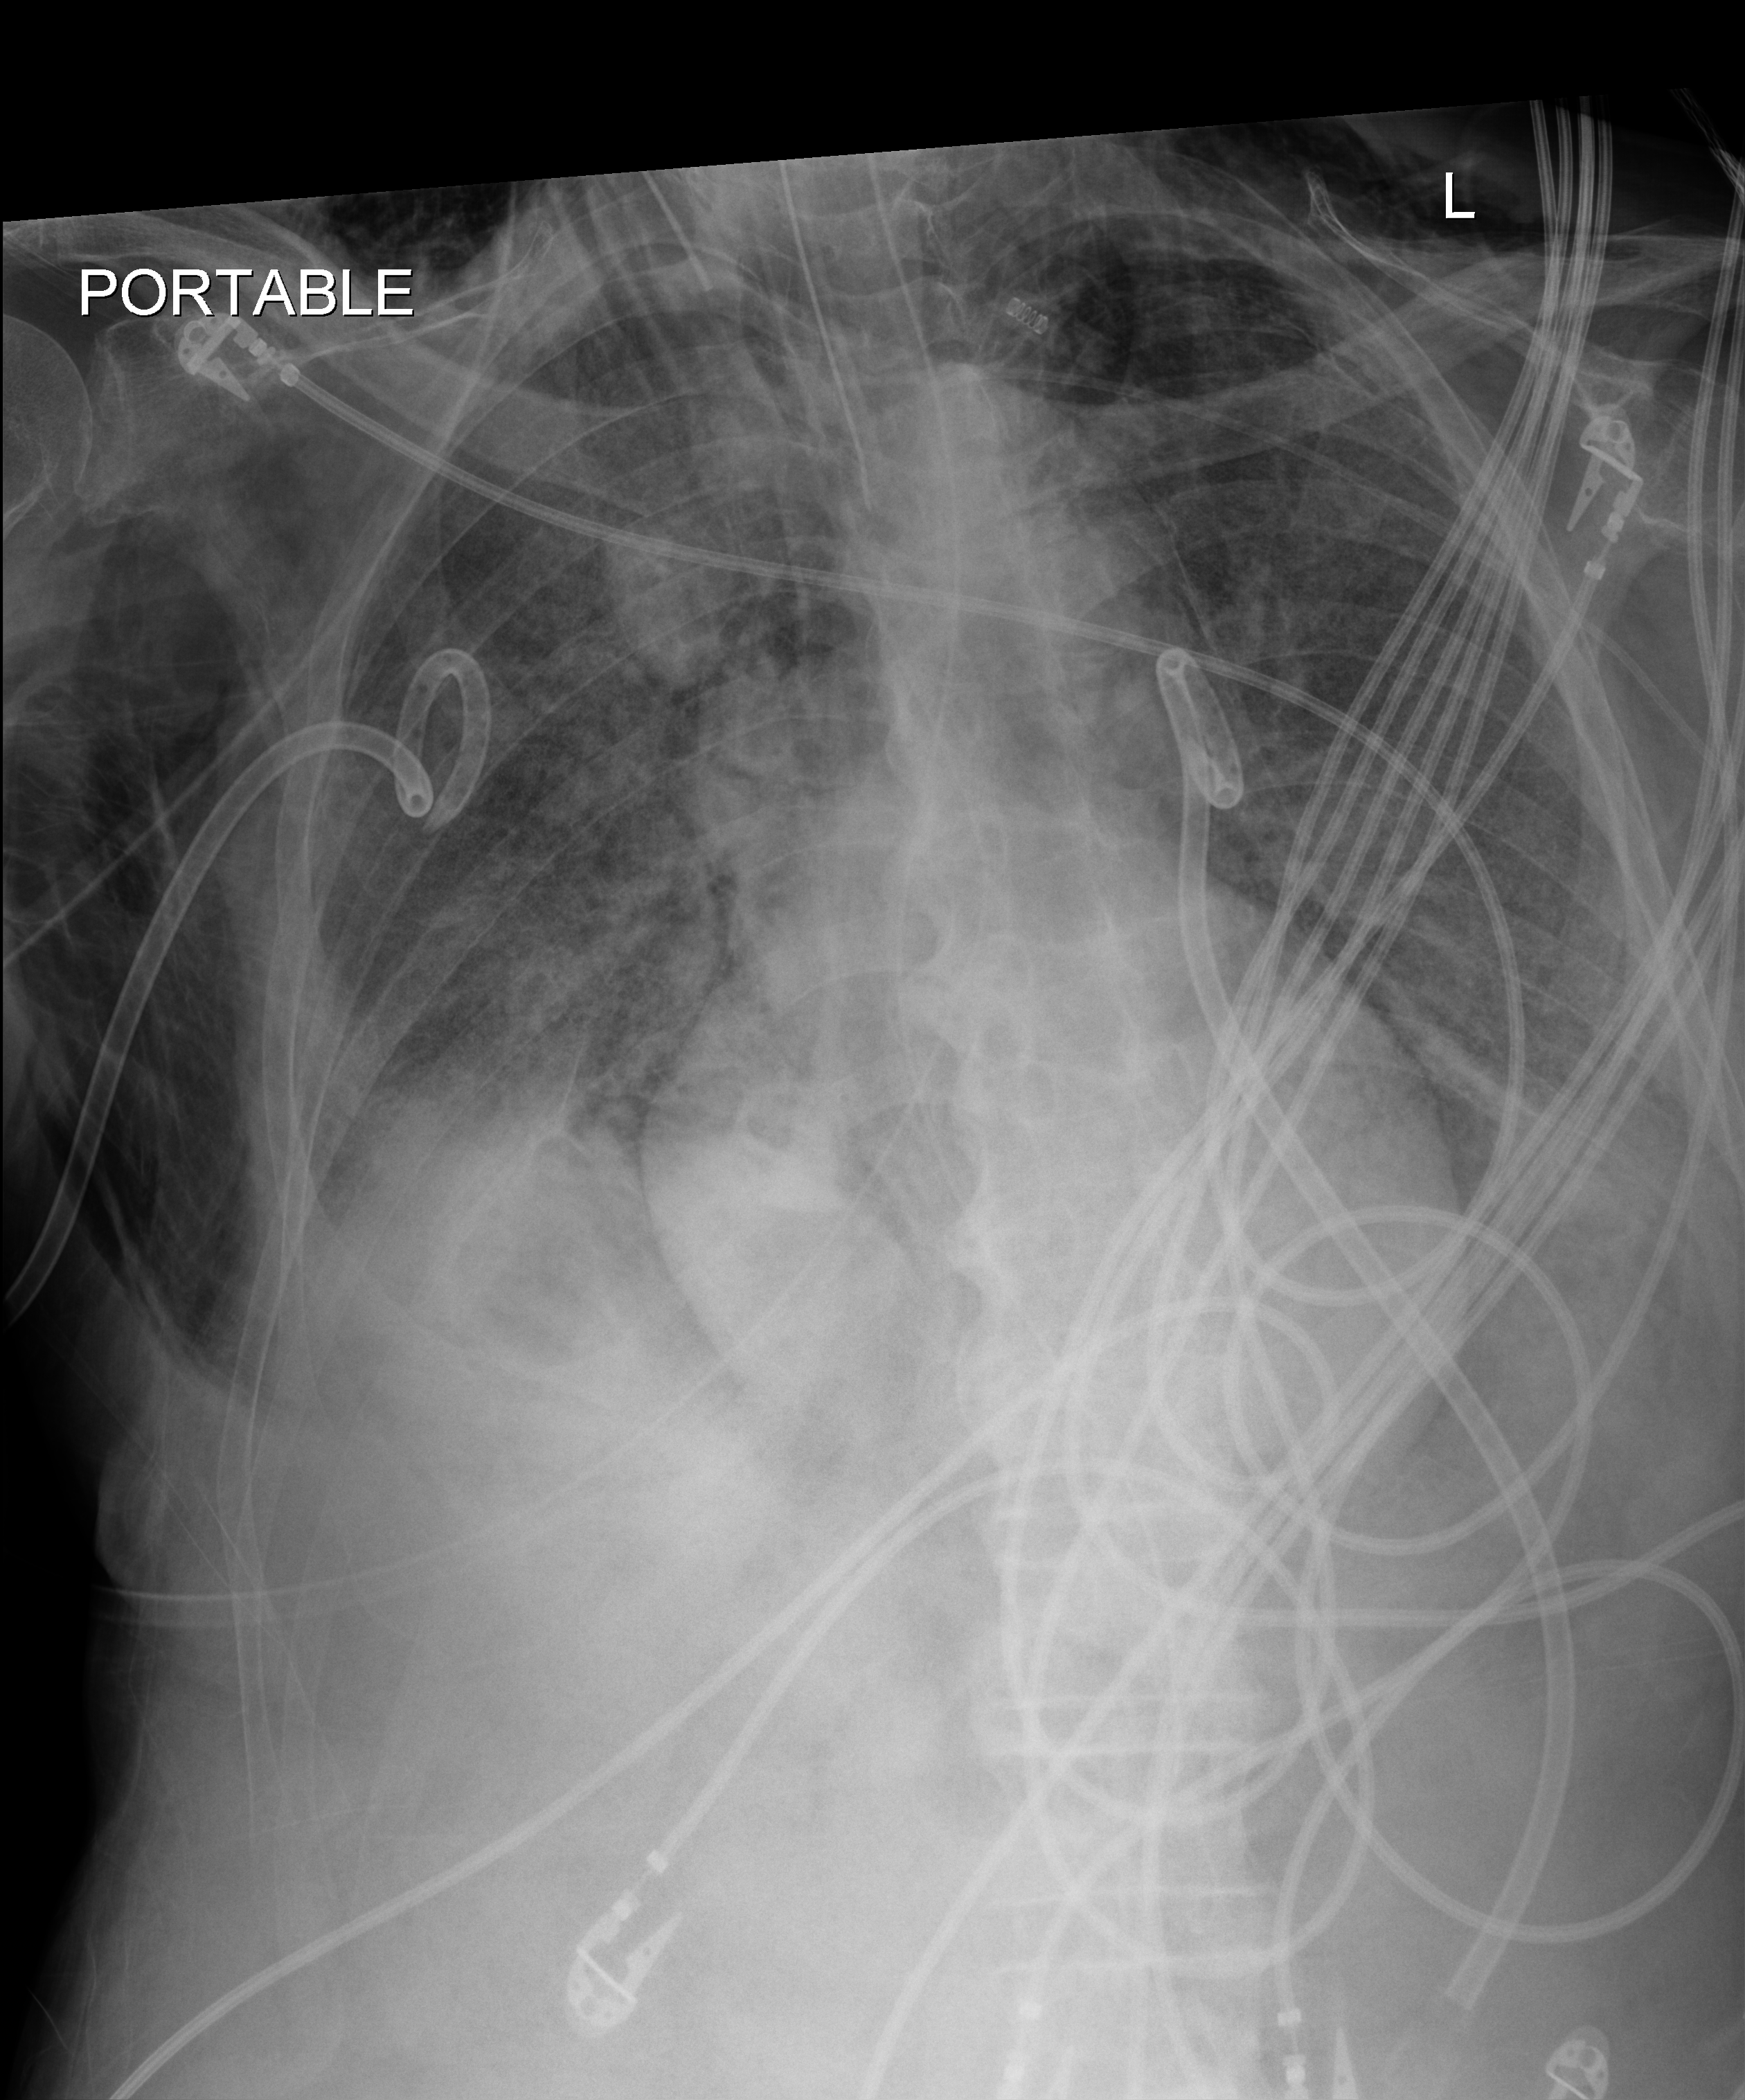
Bedside chest radiograph (digital radiography); anteroposterior (AP) projection. Male patient hospitalised with COVID-19, age 75–90 years.
Admission-level facts for this patient (not findings on this image; timing relative to this image not recorded): length of hospital stay: 30 days; admitted to intensive care during this hospital stay: yes; diabetes (admission record): no.